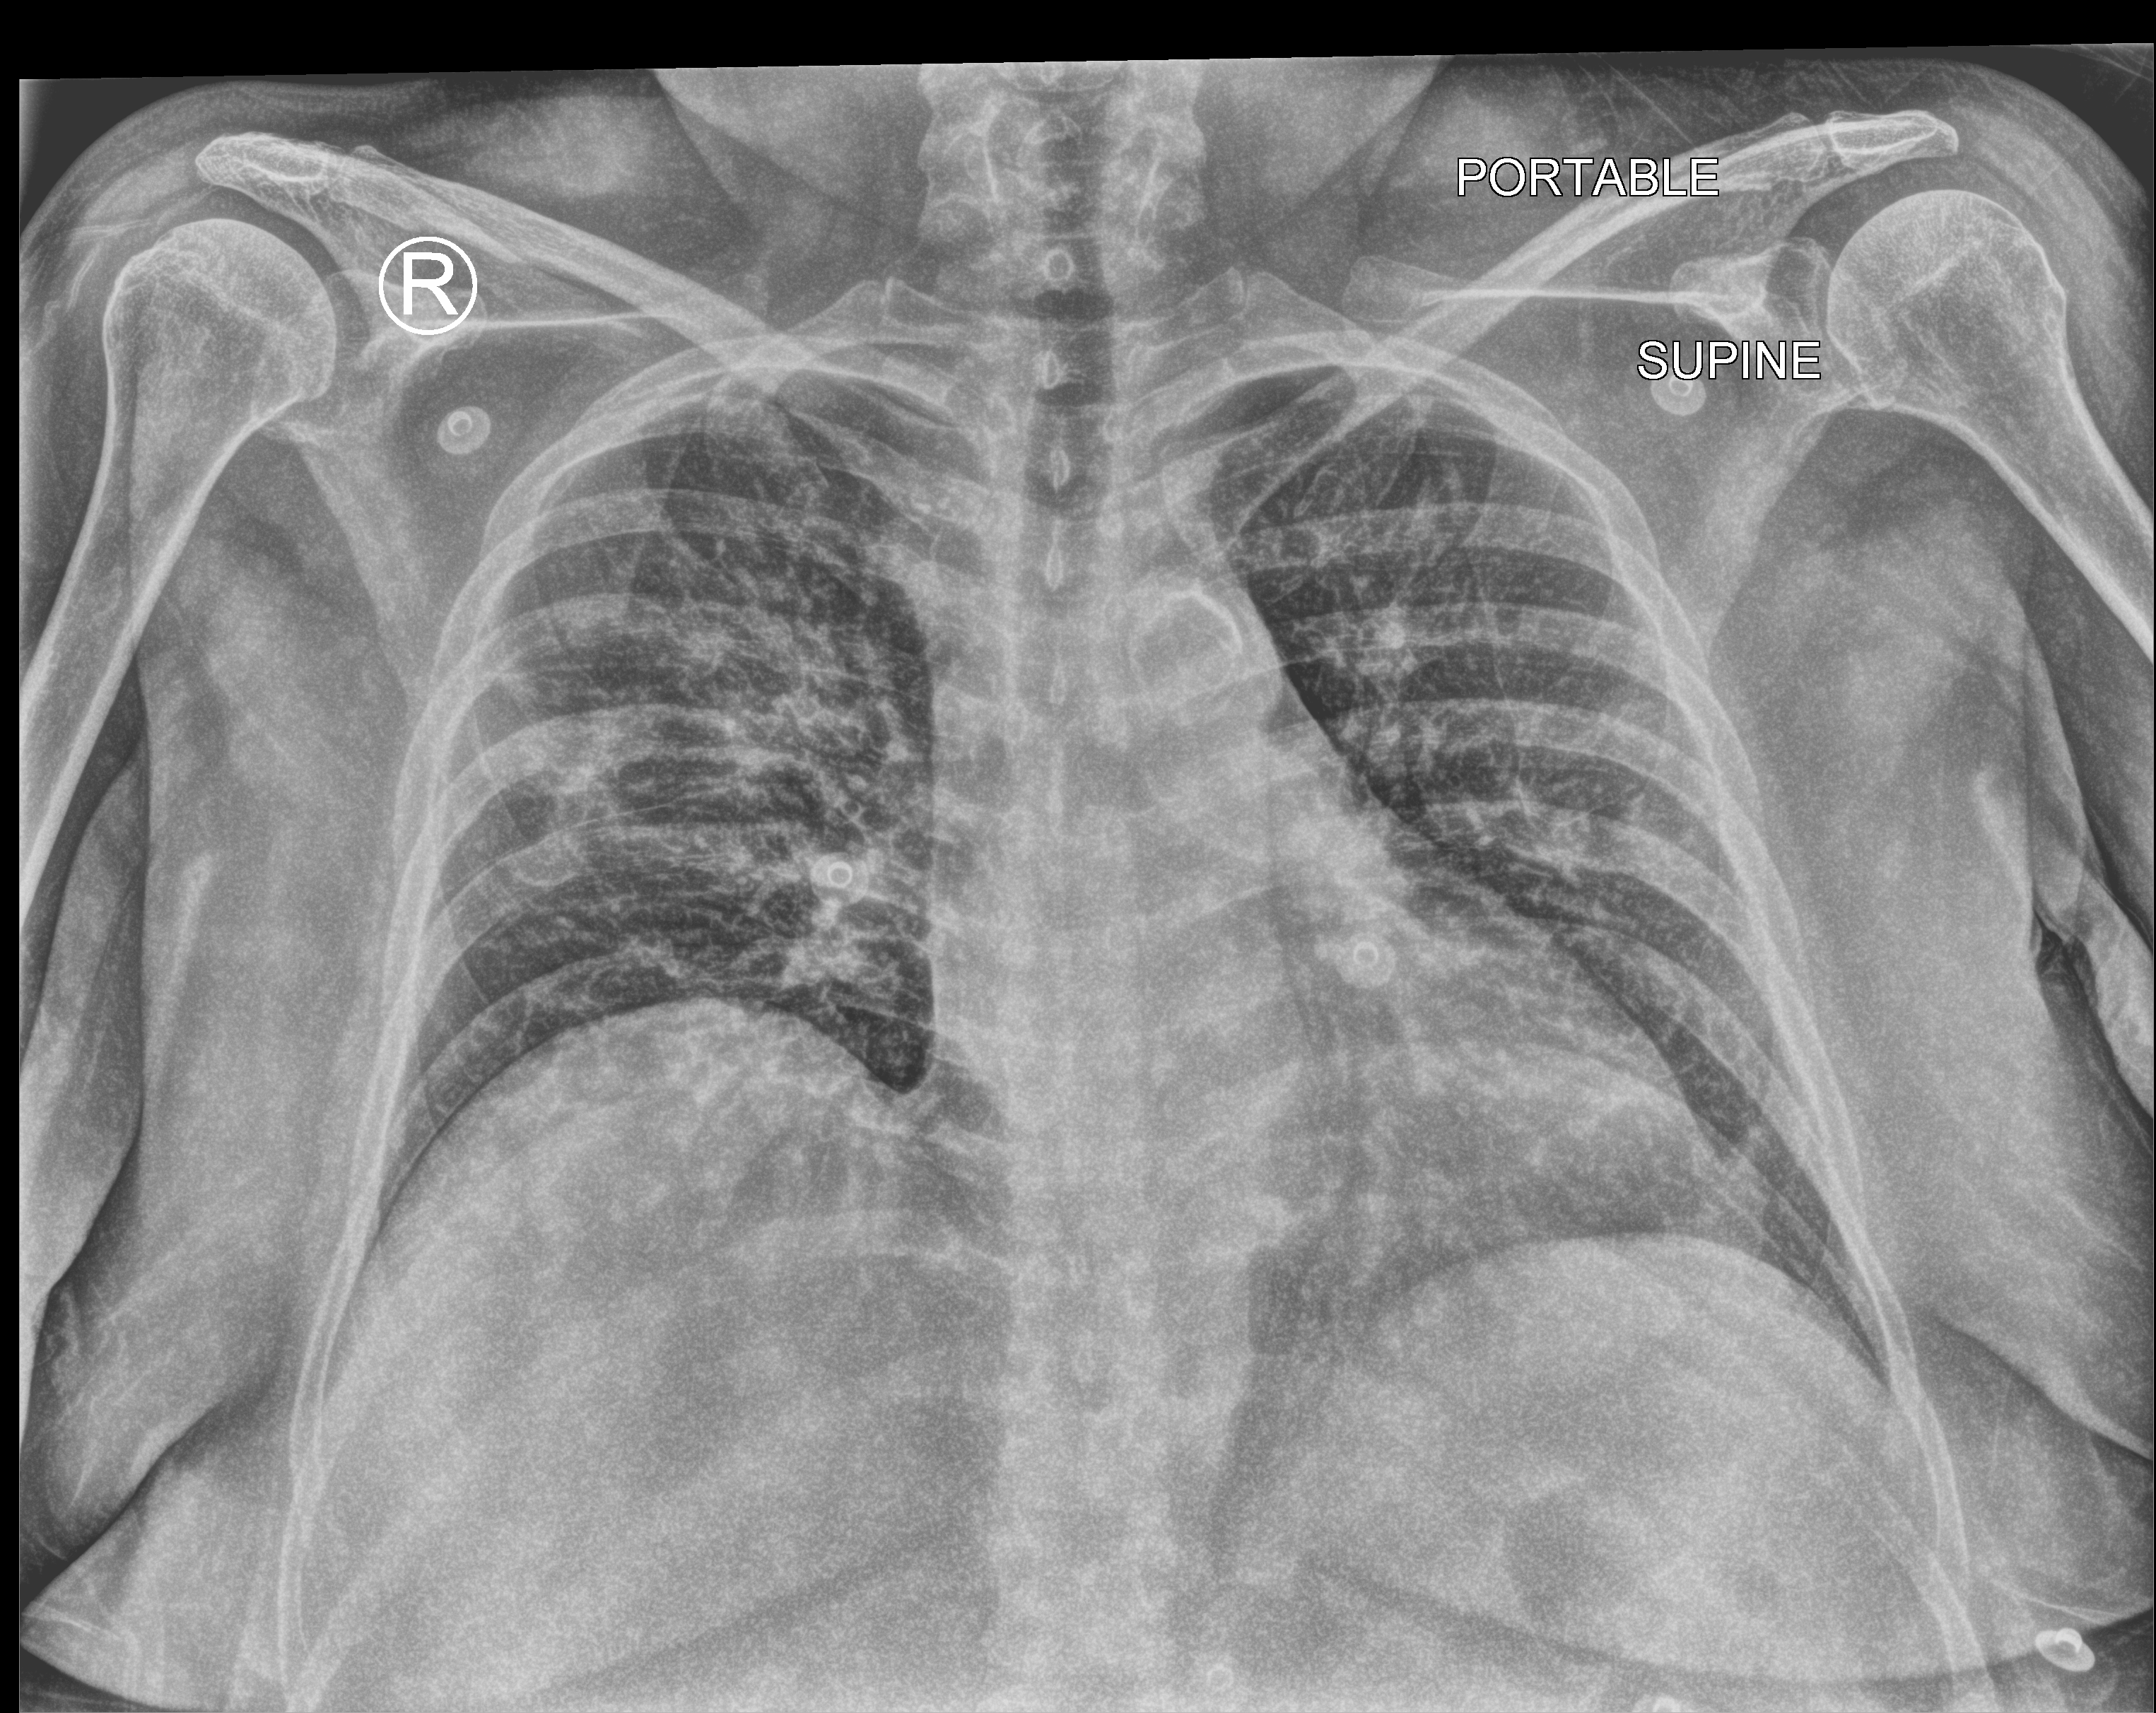
Bedside chest radiograph (computed radiography), anteroposterior (AP) projection. Female patient hospitalised with COVID-19, age 60–74 years.
From the hospital-stay record, not from the radiograph (when in the stay this image was taken is not recorded): admitted to intensive care during this hospital stay: no; mechanically ventilated during this hospital stay: no; length of hospital stay: 8 days.